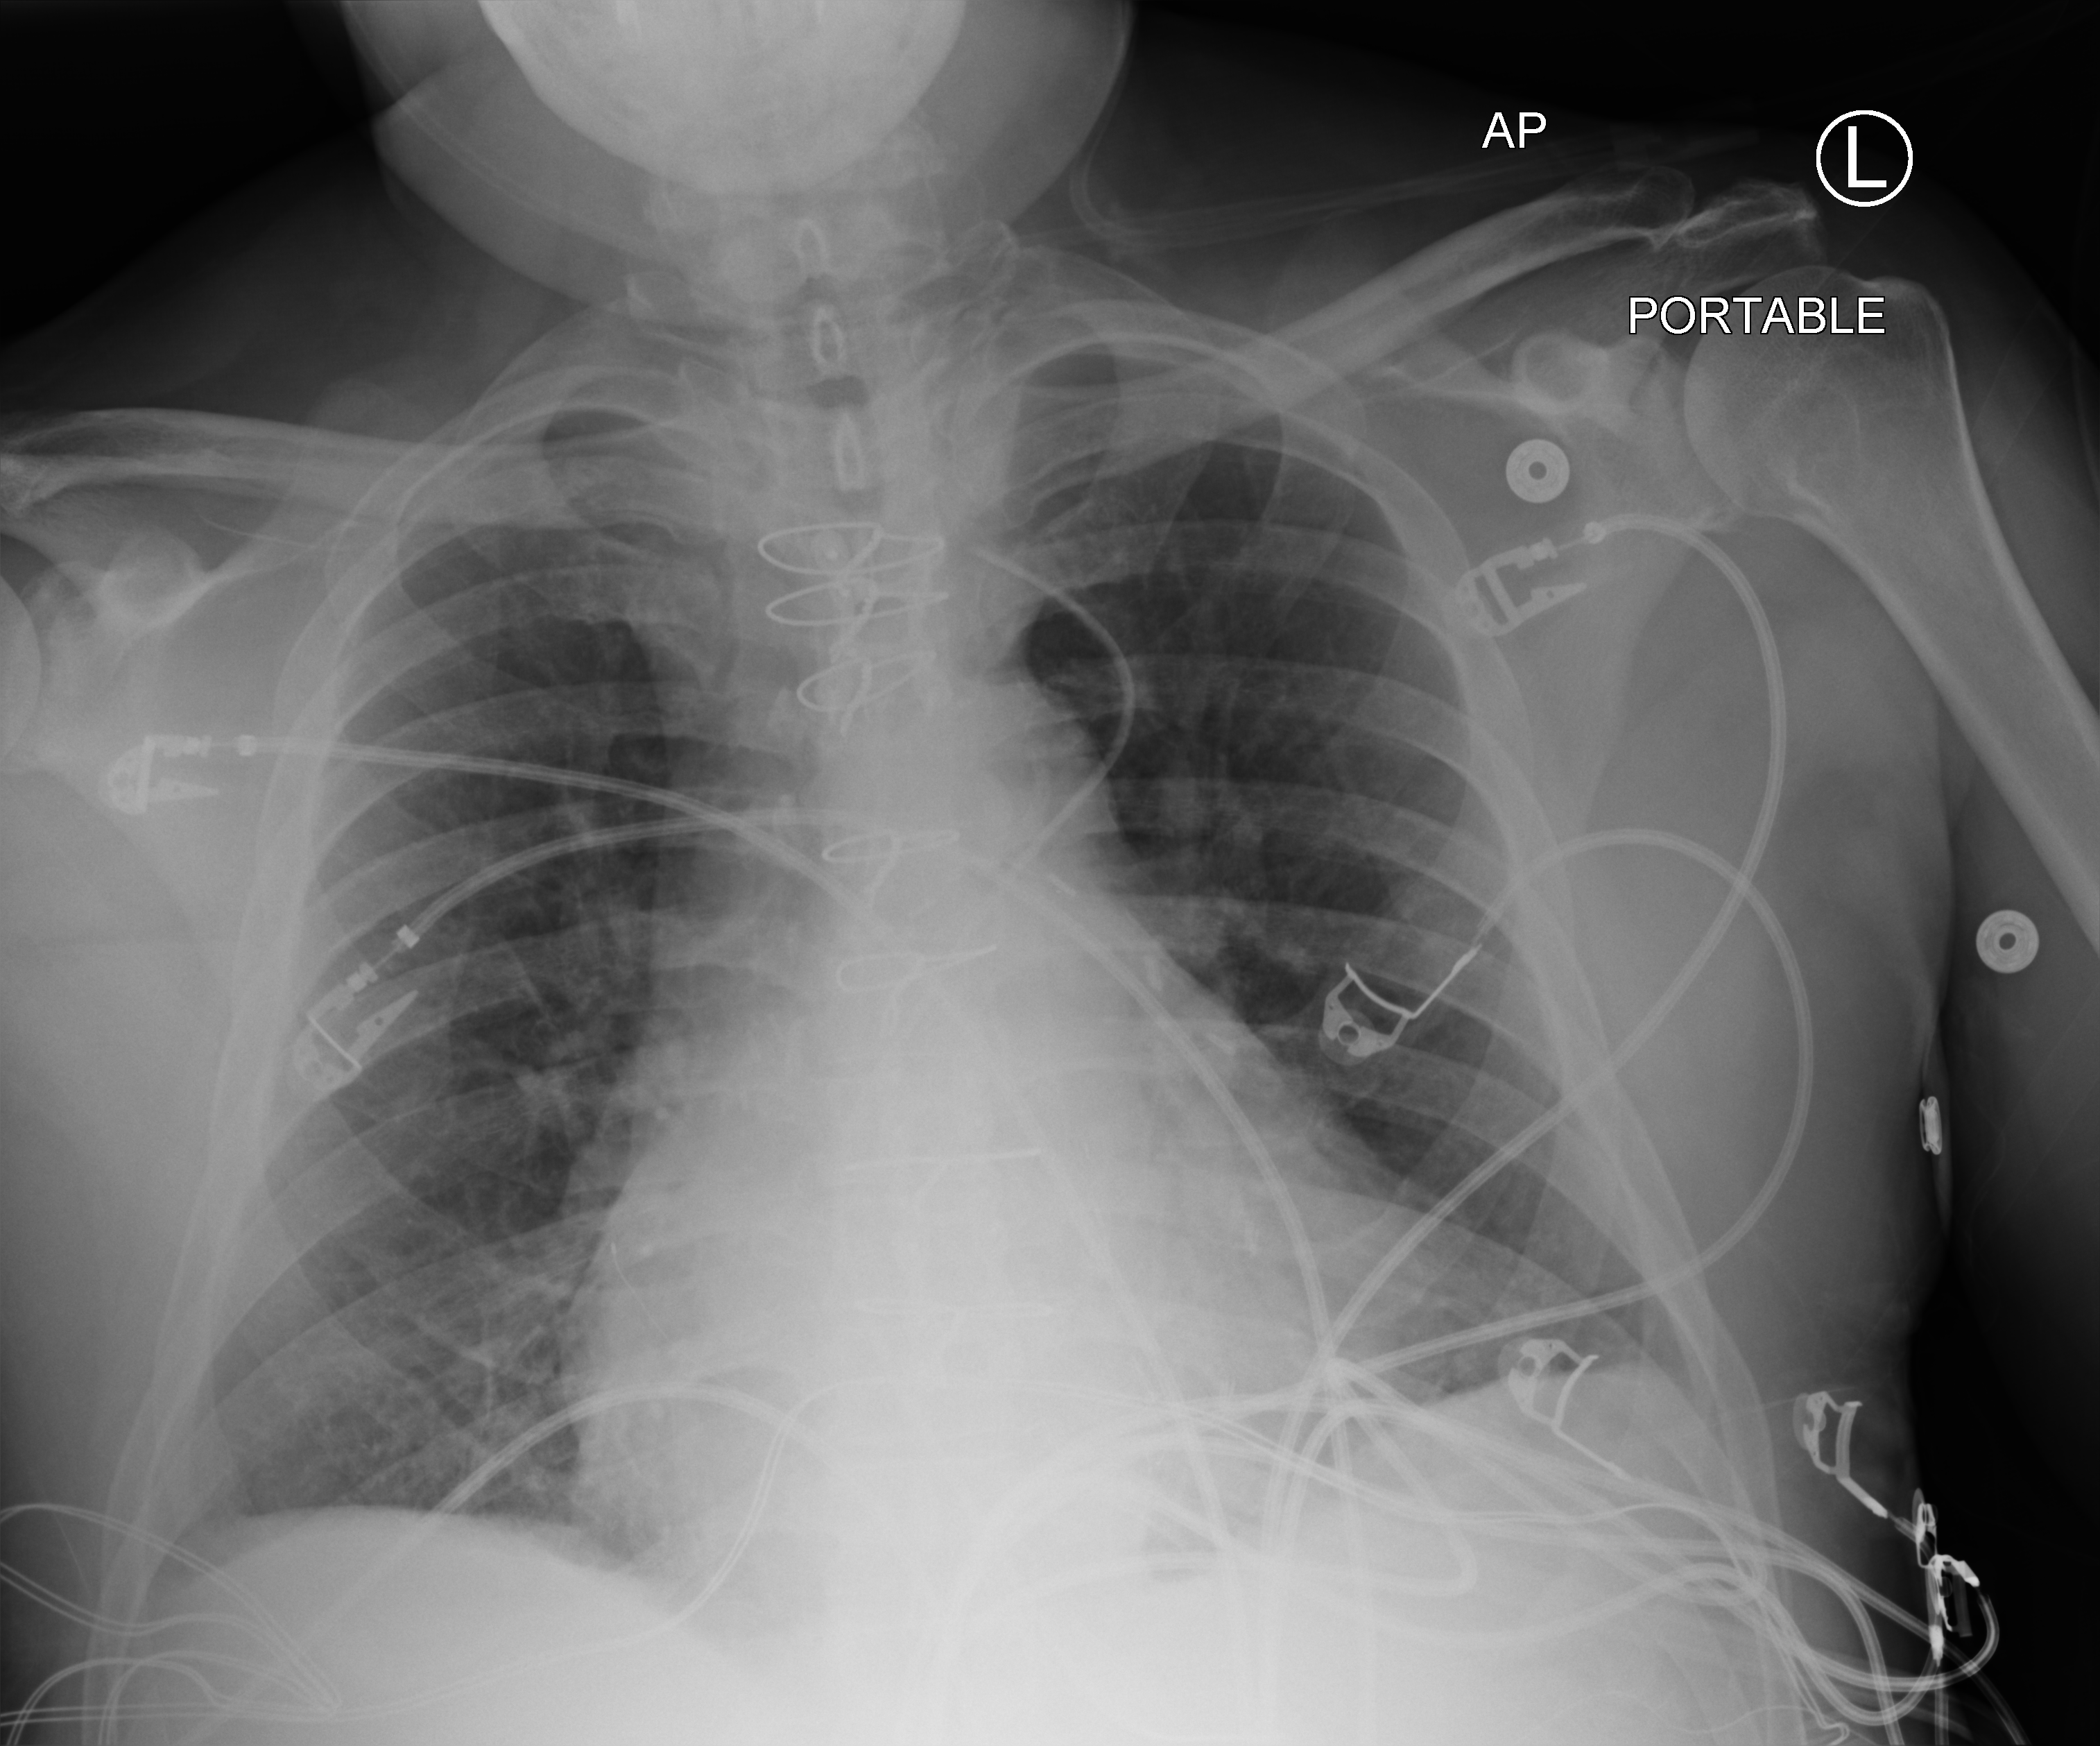
Portable chest radiograph, anteroposterior (AP) projection. Patient hospitalised with COVID-19; male, aged 60–74 years.
From the hospital-stay record, not from the radiograph (when in the stay this image was taken is not recorded): other chronic lung disease (admission record): yes; COPD (admission record): no.